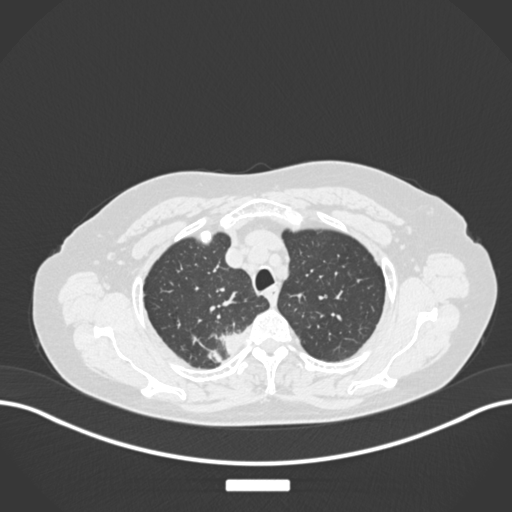
Chest CT, one axial slice. Slice 212 of 237 in the series (ordered by position). Reconstruction kernel B30f. 120 kVp. Lung window (W 1500 / L -600 HU). 1 mm slice thickness. 512 × 512 image matrix, field of view 400 × 400 mm. Patient: female, 62 years. From the clinical record (not read from this slice): clinical TNM (as recorded): T1c N1 M0.
Annotated regions visible in this slice (rectangle marked by the reading radiologist):
- lung tumour (recorded histology: squamous cell carcinoma): box from (x=202, y=331) to (x=250, y=365) px